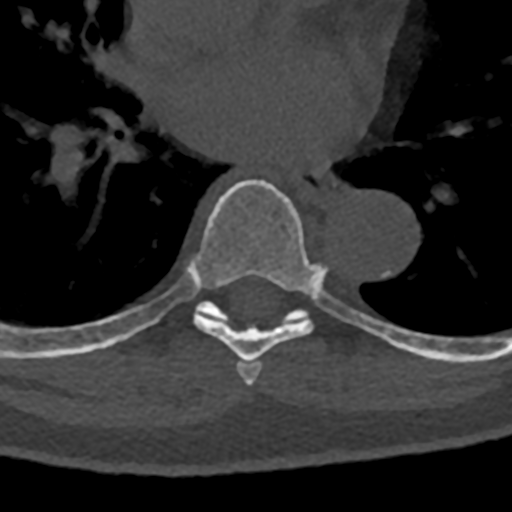
CT including the spine, one axial slice; position 751 of 797 along the scan axis; 120 kVp; bone window (W 1800 / L 400 HU); 0.5 mm slice thickness; 512 × 512 image matrix, field of view 160 × 160 mm. Patient: male, 74 years. Case-level facts recorded for this patient, not image findings: primary cancer: renal; vertebrae with lytic lesions (as recorded): T10, L1, L2, L3, L4, L5.
Outlined on this slice (semi-automatic segmentation, software-assisted and operator-edited):
- T6 vertebra: bounding box [x1, y1, x2, y2] px = [236, 361, 262, 386]
- T7 vertebra: [71, 179, 377, 363]
- T8 vertebra: [70, 302, 432, 360]